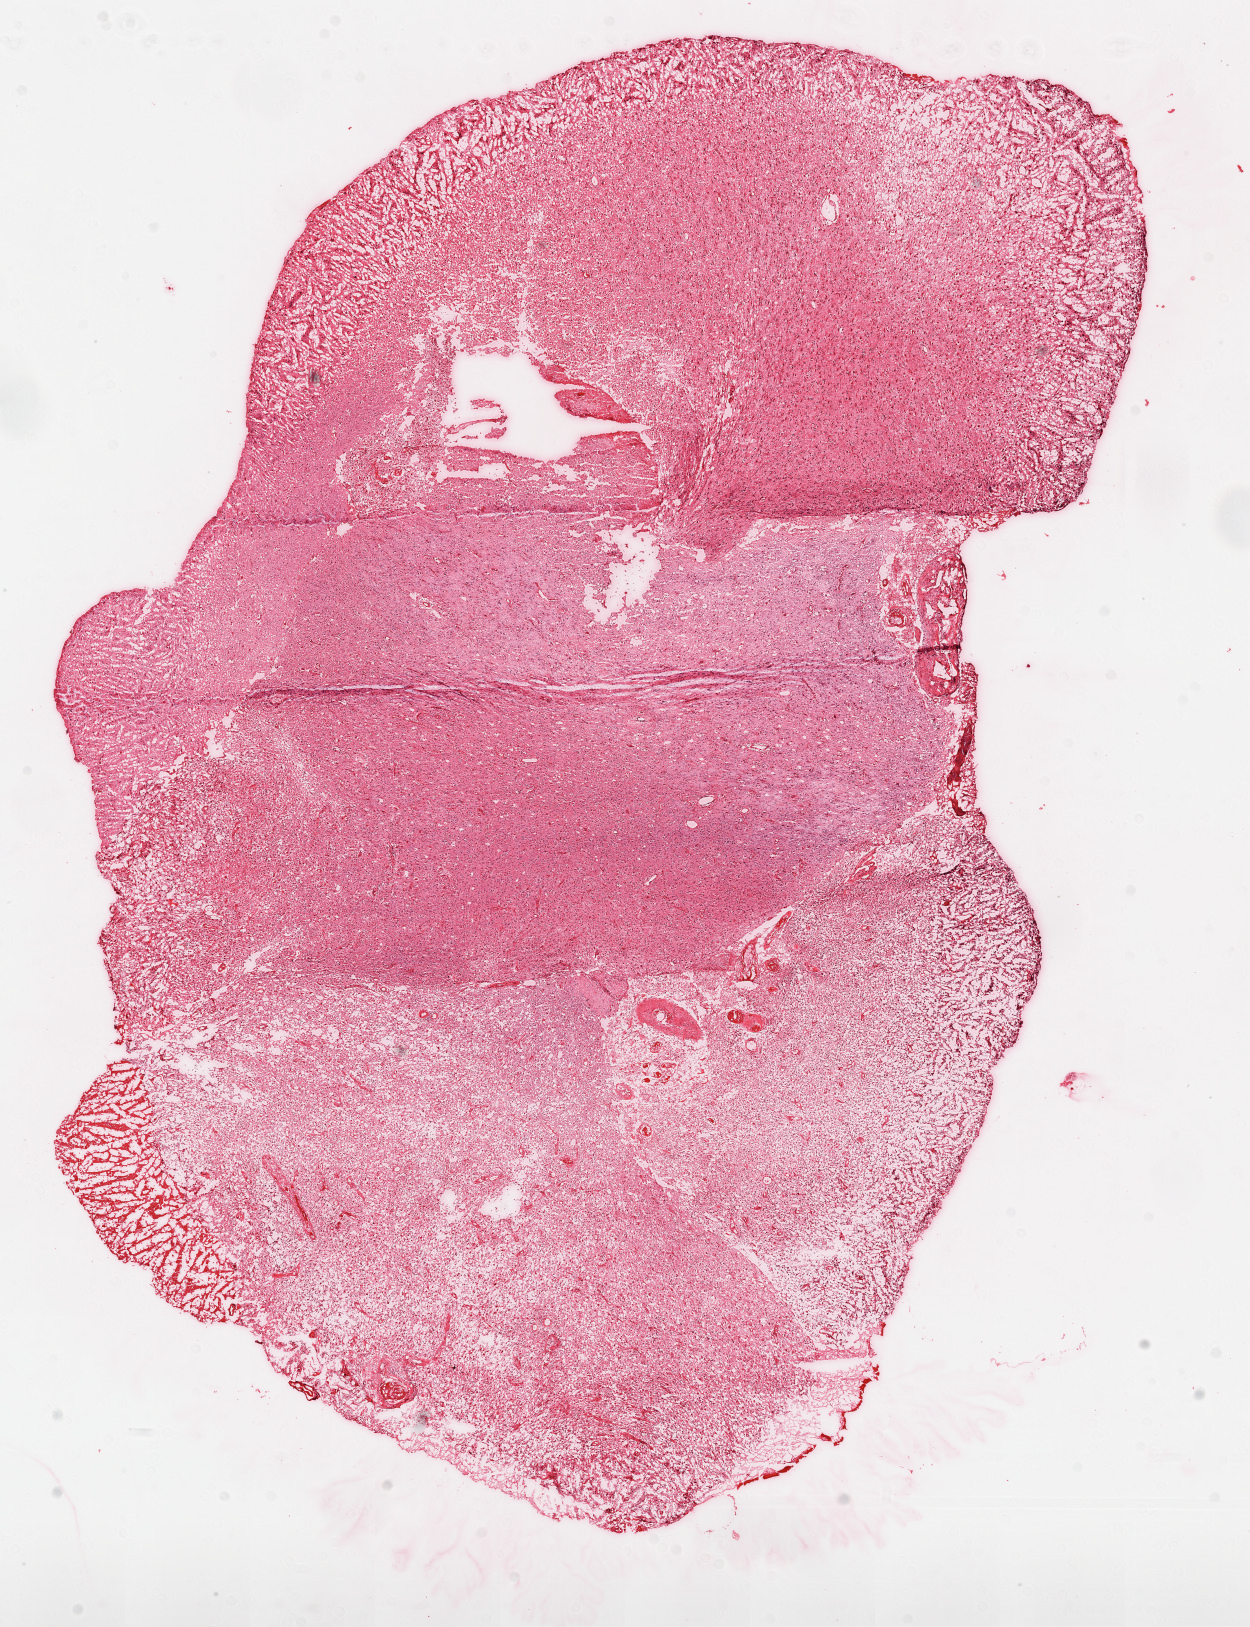
Whole-slide histology image, H&E-stained — a low-resolution overview of the entire scanned area, about 10.0 x 13.1 mm, frozen section from the top of the tissue portion, brain, primary tumour sample. Male patient; age at initial diagnosis 54 years. Slide review estimates, as recorded: tumour cells 75%, tumour nuclei 80%, stromal cells 20%, necrosis 5%.
Histologic diagnosis: Glioblastoma.